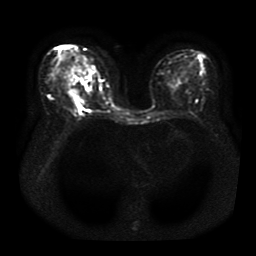
Breast MRI, one axial slice. Position 17 of 41 along the scan axis. Diffusion-weighted series; image 2 of 4 stored at this slice position (different b-values; order by instance number). 1.5 T. 5 mm slice thickness. 256 × 256 image matrix, field of view 330 × 330 mm. Female patient.
Outlined on this slice (expert manual segmentation):
- tumour on diffusion-weighted imaging: box from (x=76, y=90) to (x=79, y=95) px